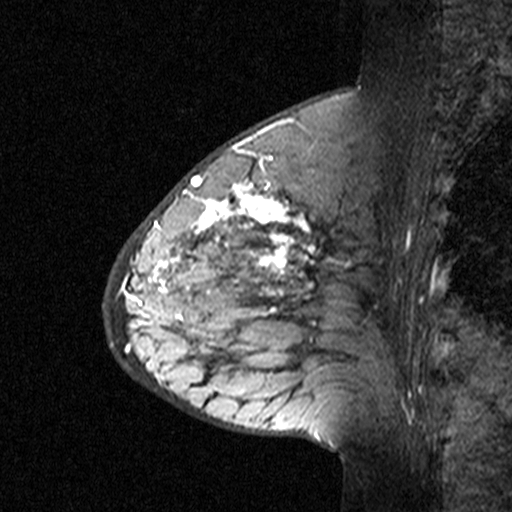
Breast MRI (dynamic contrast-enhanced), one sagittal slice; slice 15 of 44 in the series (ordered by position); dynamic contrast-enhanced study with each time point stored as its own series, time point 3 of 4 at this slice position (ordered by acquisition time); 1.5 T; TE 4.5 ms, TR 11 ms; 3 mm slice thickness; 512 × 512 image matrix, field of view 200 × 200 mm. Female patient, age 65 years. Case-level facts recorded for this patient, not image findings: setting: breast cancer imaged before/during neoadjuvant chemotherapy; receptor status: HER2-positive.
Outlined on this slice (semi-automatically segmented with operator editing):
- analysis volume of interest (the breast-tissue region the enhancement analysis was run in; not a lesion): box from (x=182, y=190) to (x=353, y=361) px
- tumour enhancement mask (voxels above the 90 % enhancement threshold inside the analysis volume of interest): (x=182, y=190)–(x=350, y=315)